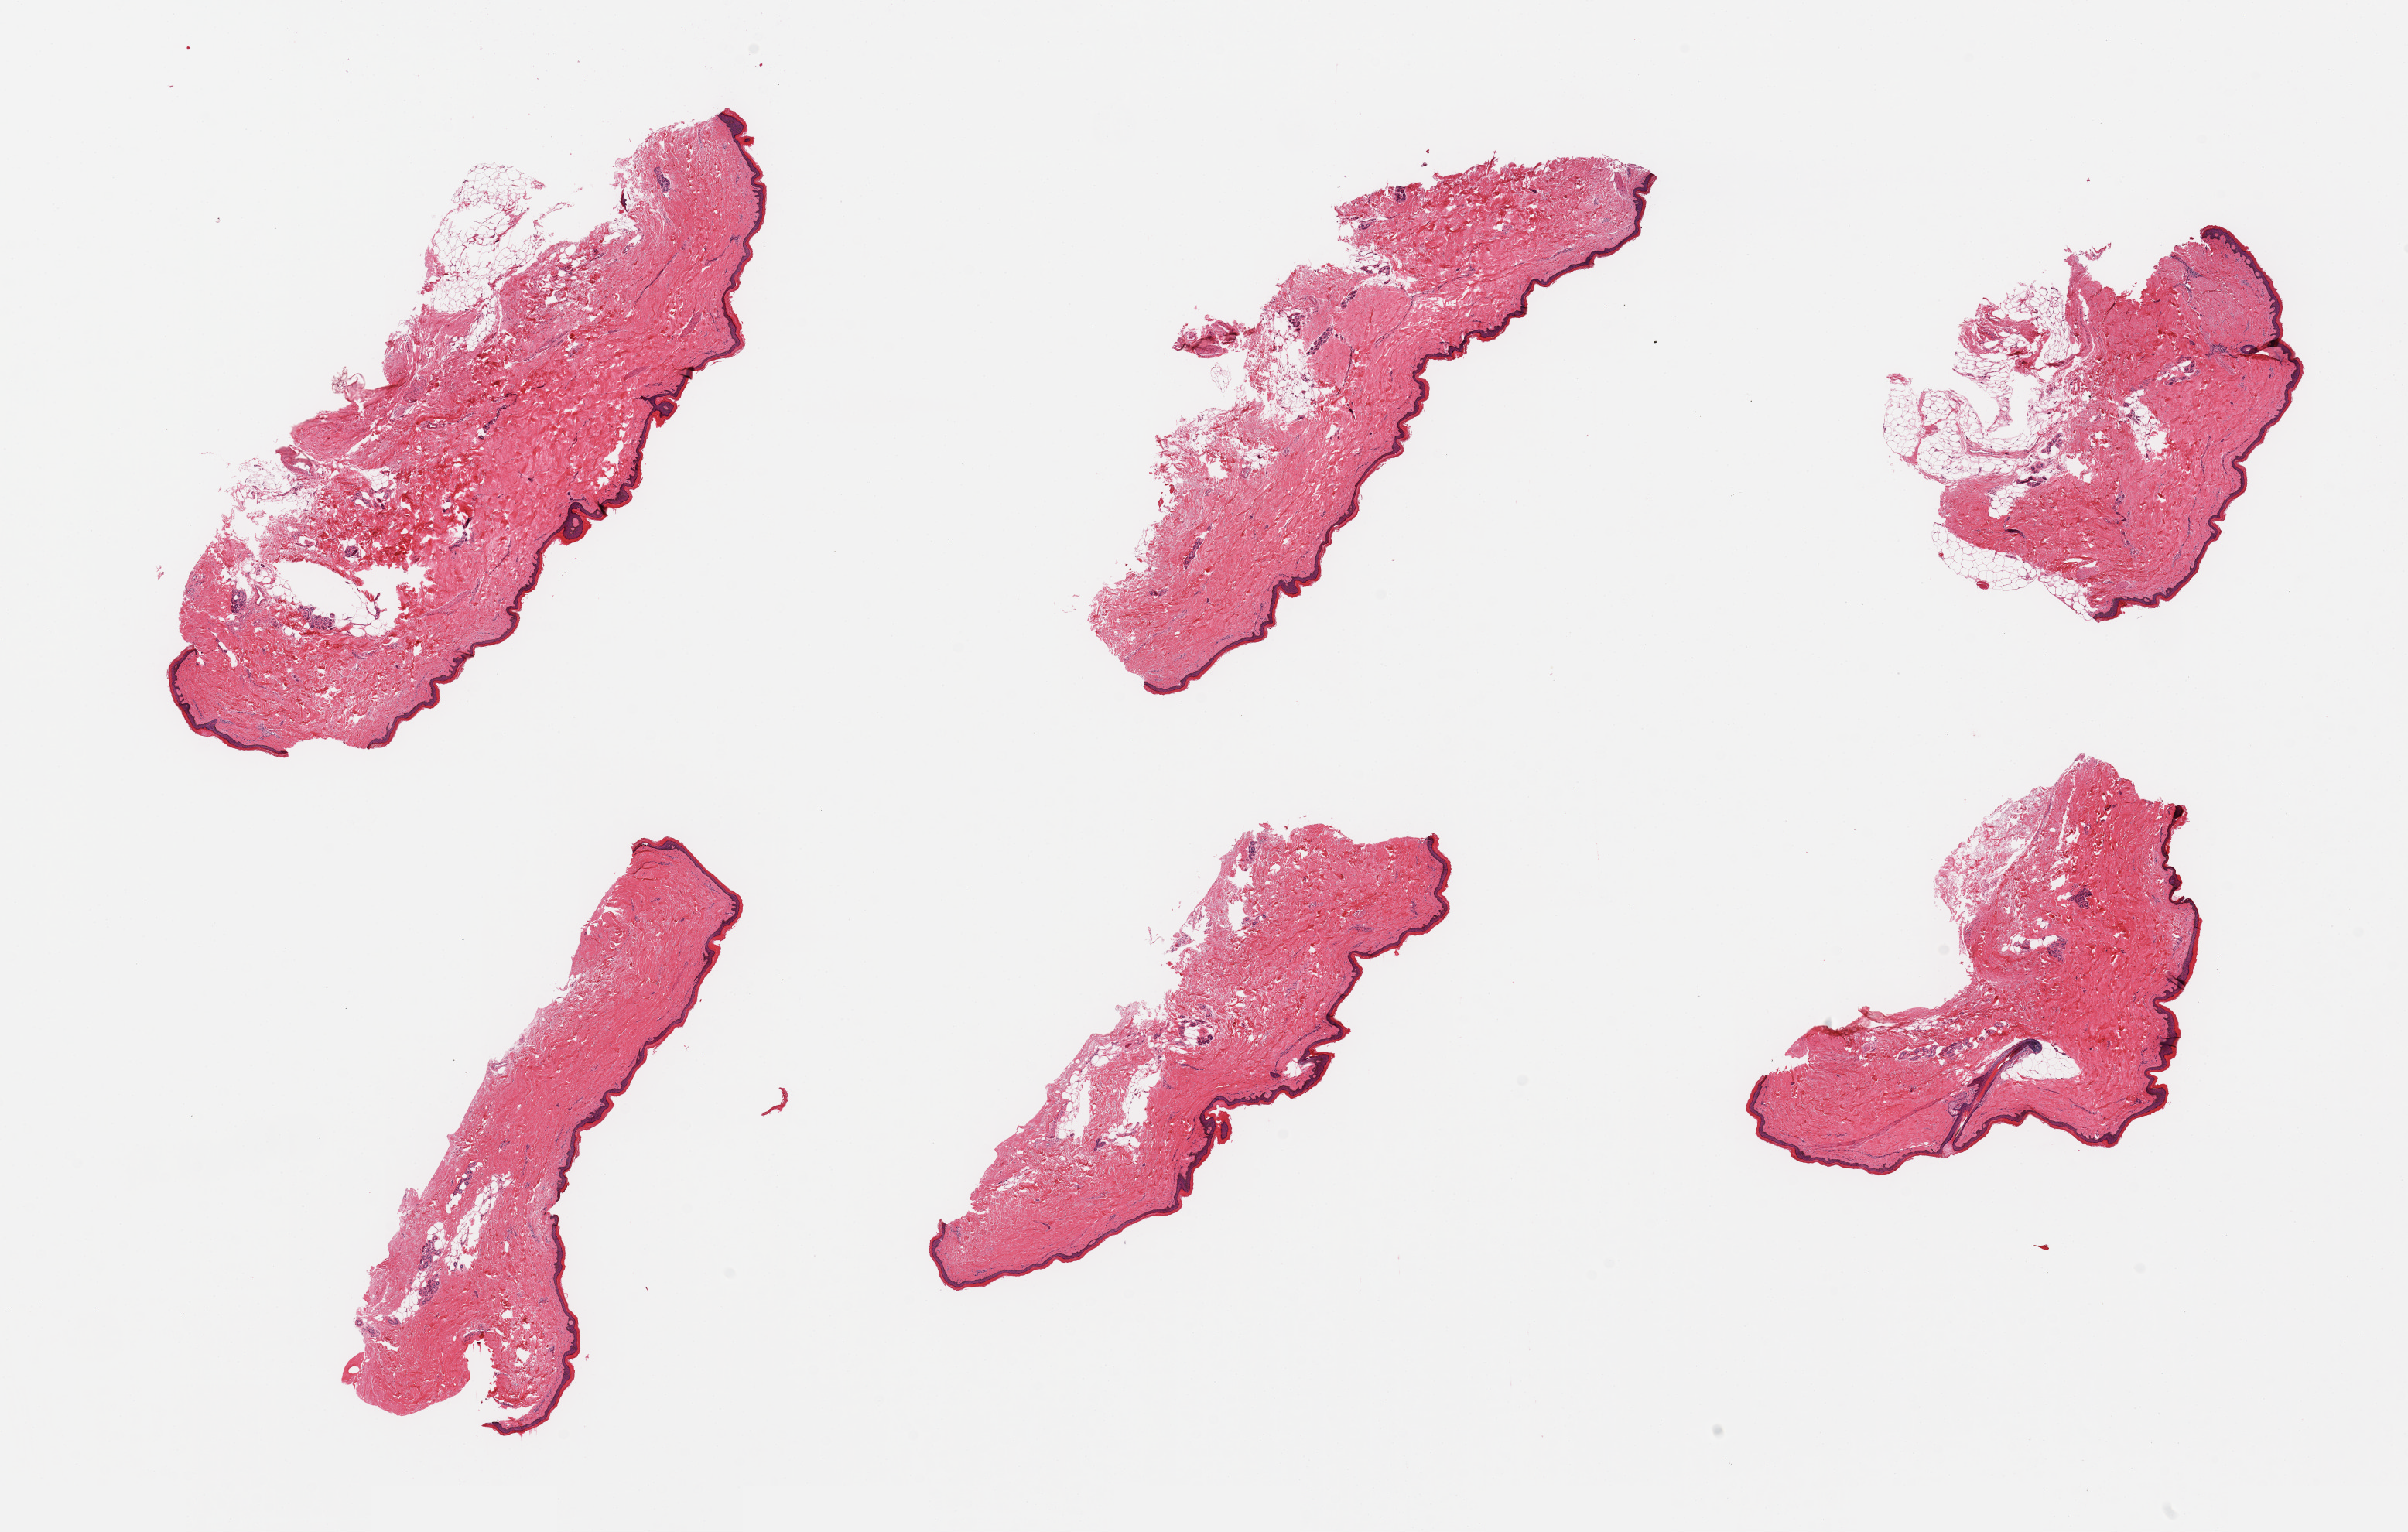
Digitized haematoxylin and eosin-stained section — a low-resolution overview of the entire scanned area, about 24.6 x 15.7 mm (slide scanned at 20x). PAXgene-fixed, paraffin-embedded tissue. Section of skin of lower leg (target tissue). Donor tissue sample. Female donor.
Review note (as recorded): 6 pieces: 1 with excess subcutaneous fat; others well trimmed.